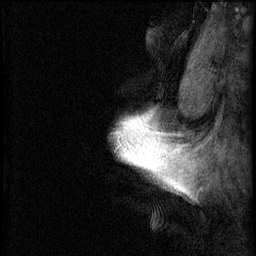
Breast MRI (dynamic contrast-enhanced), one sagittal slice; position 56 of 60 along the scan axis; 3 images stored at this slice position (order not interpretable as contrast timing); 1.5 T; TE 4.2 ms, TR 8.2 ms; 2 mm slice thickness; 256 × 256 image matrix, field of view 180 × 180 mm. Patient: female, 40 years.
Outlined on this slice (semi-automatically segmented with operator editing):
- analysis volume of interest (the breast-tissue region the enhancement analysis was run in; not a lesion): box from (x=118, y=110) to (x=167, y=187) px
- tumour enhancement mask (voxels above the 70 % enhancement threshold inside the analysis volume of interest): (x=119, y=114)–(x=167, y=183)